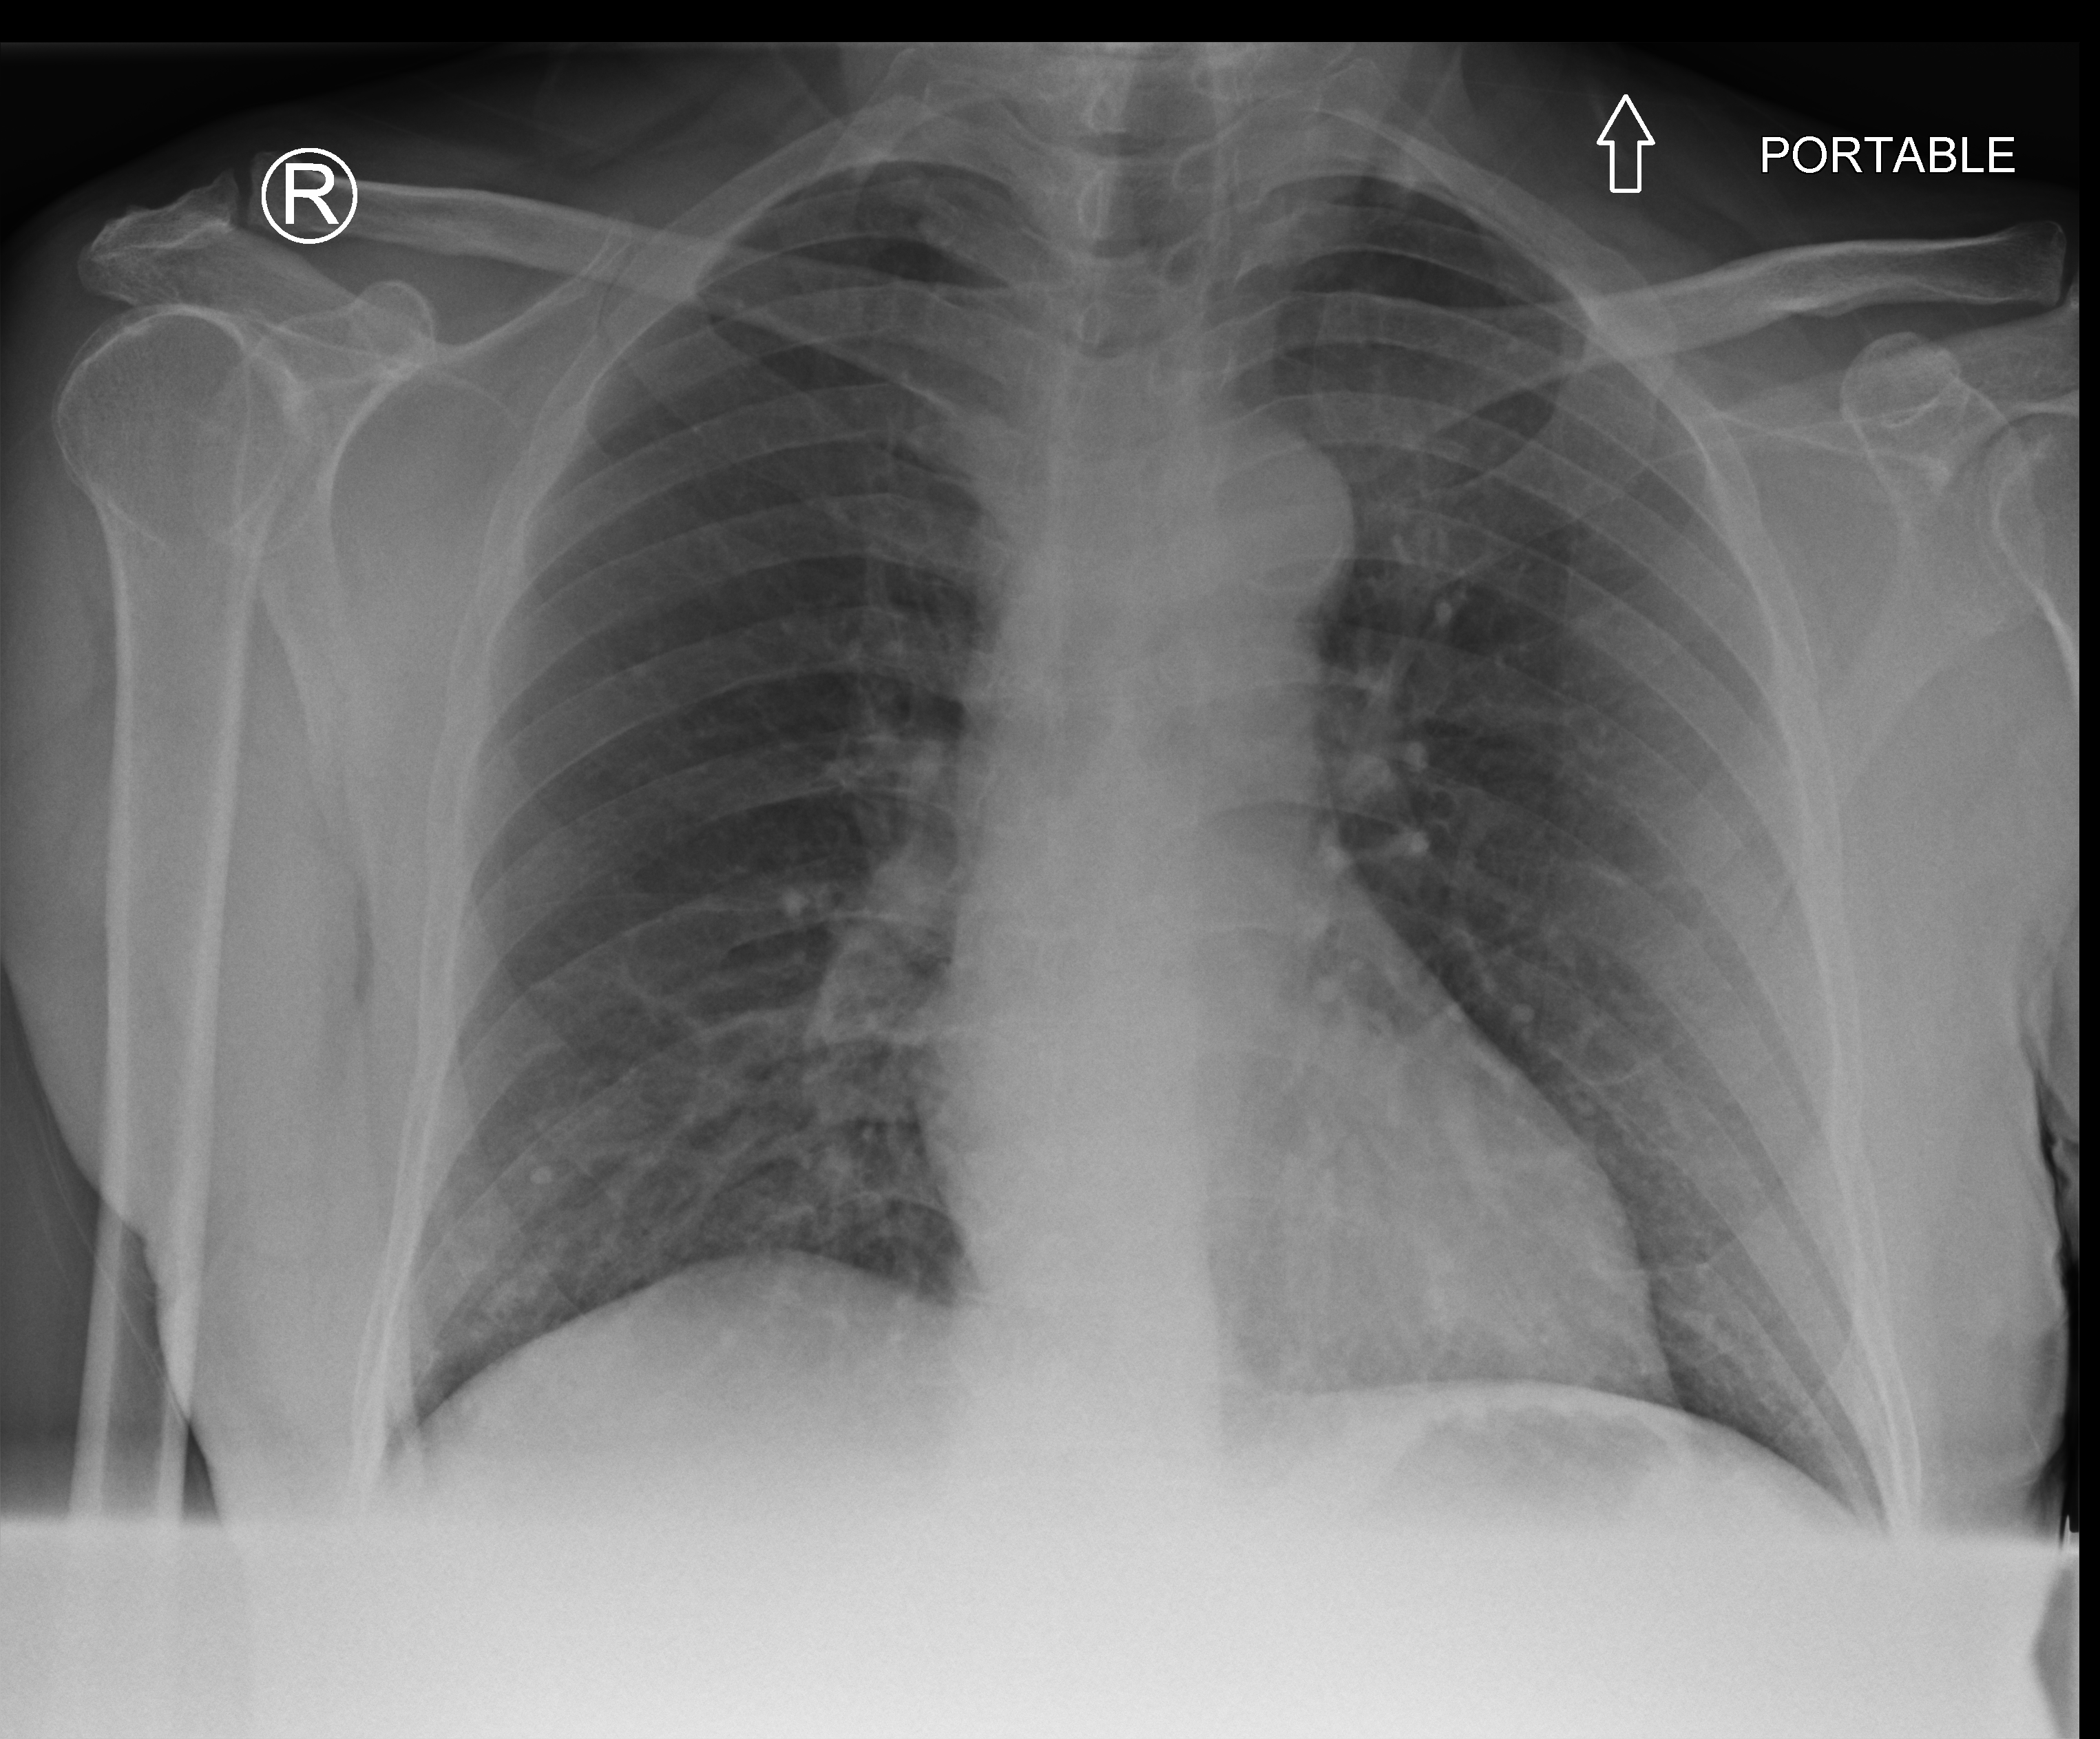
Bedside chest radiograph (computed radiography), anteroposterior (AP) projection. Male patient hospitalised with COVID-19, age 60–74 years.
Hospital-stay facts (about this admission, not read from this image; timing relative to this image not recorded): mechanically ventilated during this hospital stay: no; admitted to intensive care during this hospital stay: no.